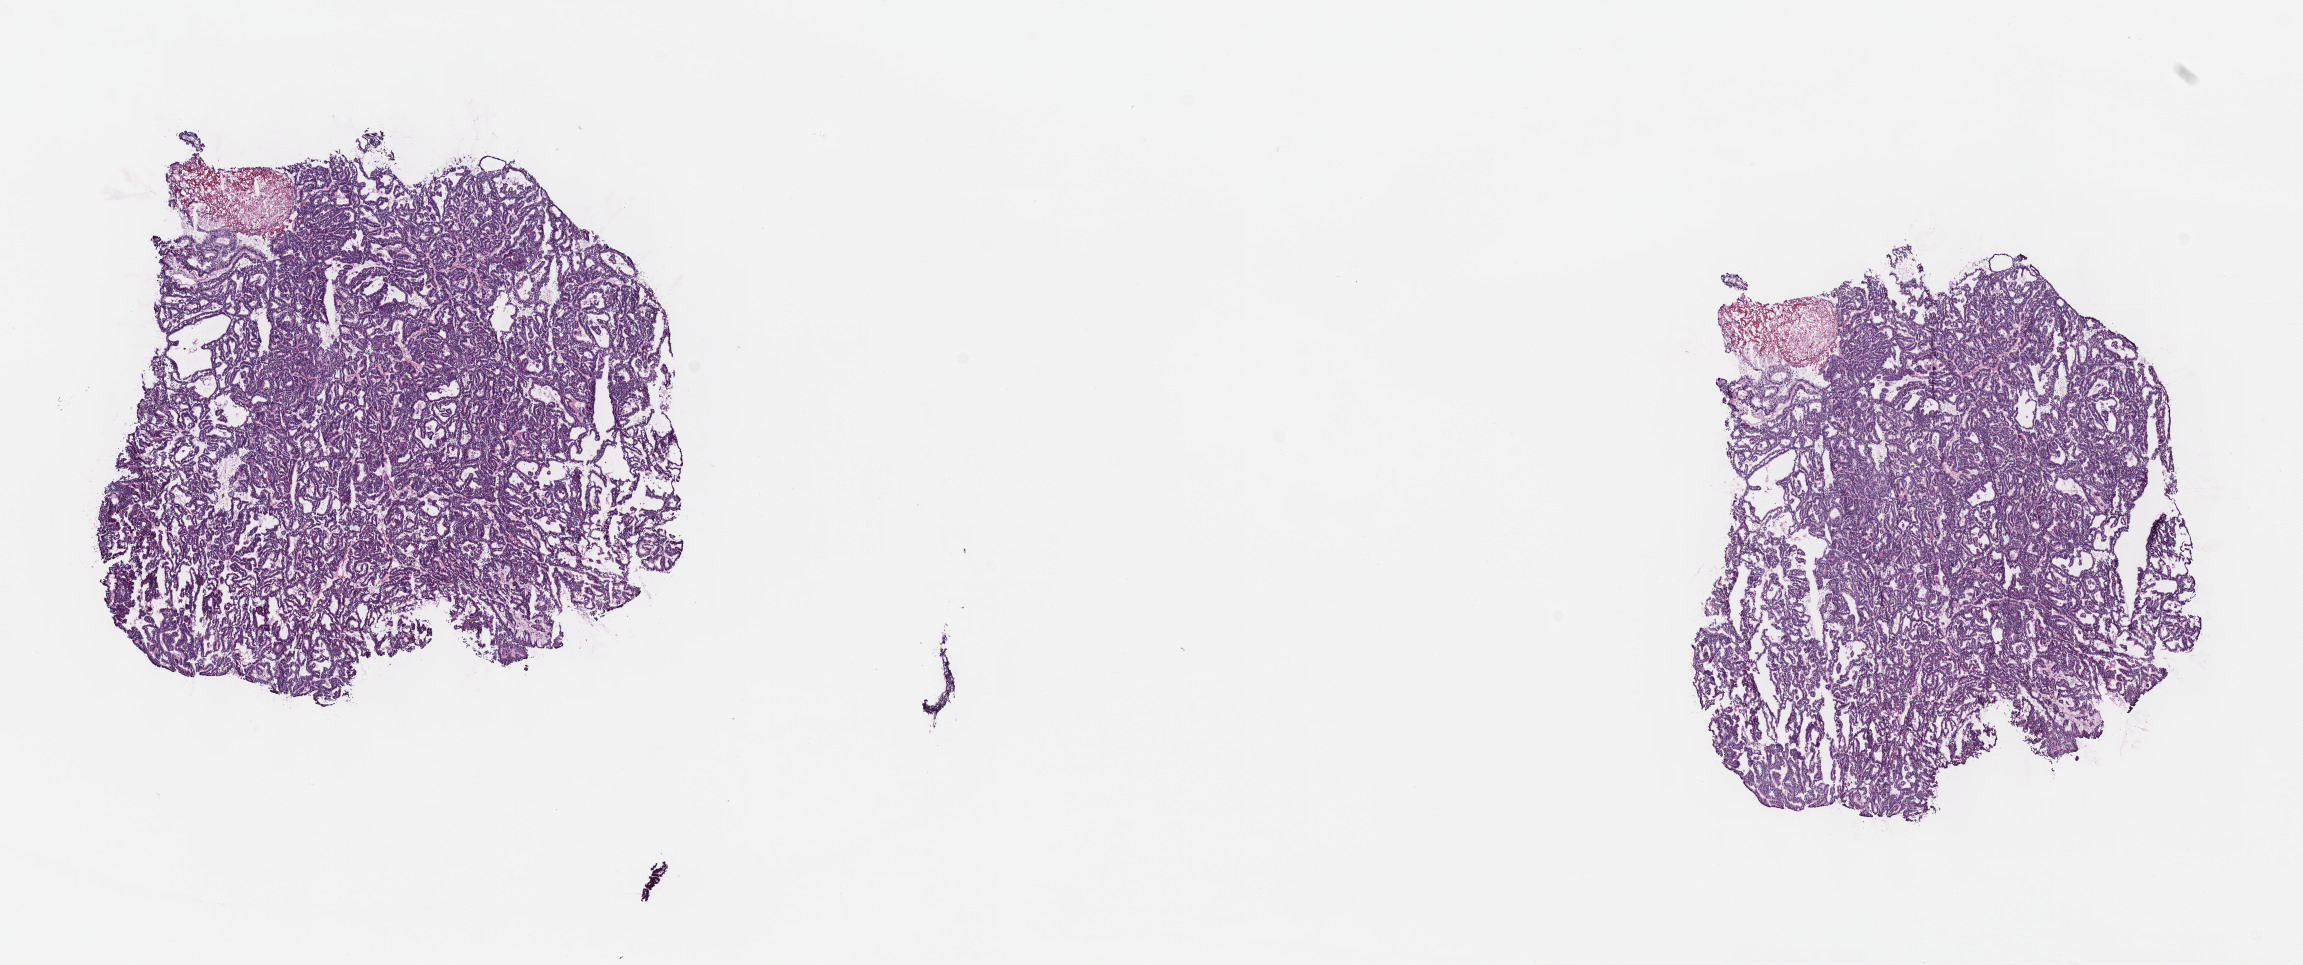
Digitized Hematoxylin and eosin (H&E) stained tissue section (whole slide), whole scanned area (about 18.6 x 7.8 mm, slide scanned at 40x) shown as a low-resolution overview. Frozen section from the top of the tissue portion. Kidney, primary tumour sample. Female, age 57 years at initial diagnosis. Pathologist review of this section (percent, as recorded): tumour cells 75%, tumour nuclei 75%, normal cells 0%, stromal cells 18%, necrosis 7%. Infiltration values recorded for this section: lymphocyte infiltration 2%, monocyte infiltration 5%, neutrophil infiltration 1%.
TNM: T1a NX MX. AJCC pathologic stage: I (7th edition). Histologic diagnosis: Papillary adenocarcinoma, NOS.